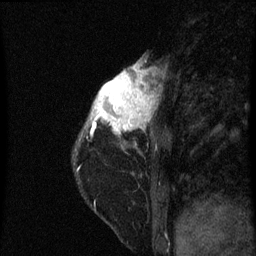
Breast MRI (dynamic contrast-enhanced), one sagittal slice; slice 17 of 60 in the series (ordered by position); dynamic contrast-enhanced series, image 2 of 3 at this slice position (ordered by acquisition); 1.5 T; TE 4.2 ms, TR 8 ms; 2 mm slice thickness; 256 × 256 image matrix. Patient: female, 38 years.
Annotated regions visible in this slice (semi-automatic segmentation, software-assisted and operator-edited):
- analysis volume of interest (the breast-tissue region the enhancement analysis was run in; not a lesion): box from (x=80, y=64) to (x=157, y=151) px
- tumour enhancement mask (voxels above the 70 % enhancement threshold inside the analysis volume of interest): (x=92, y=64)–(x=153, y=135)